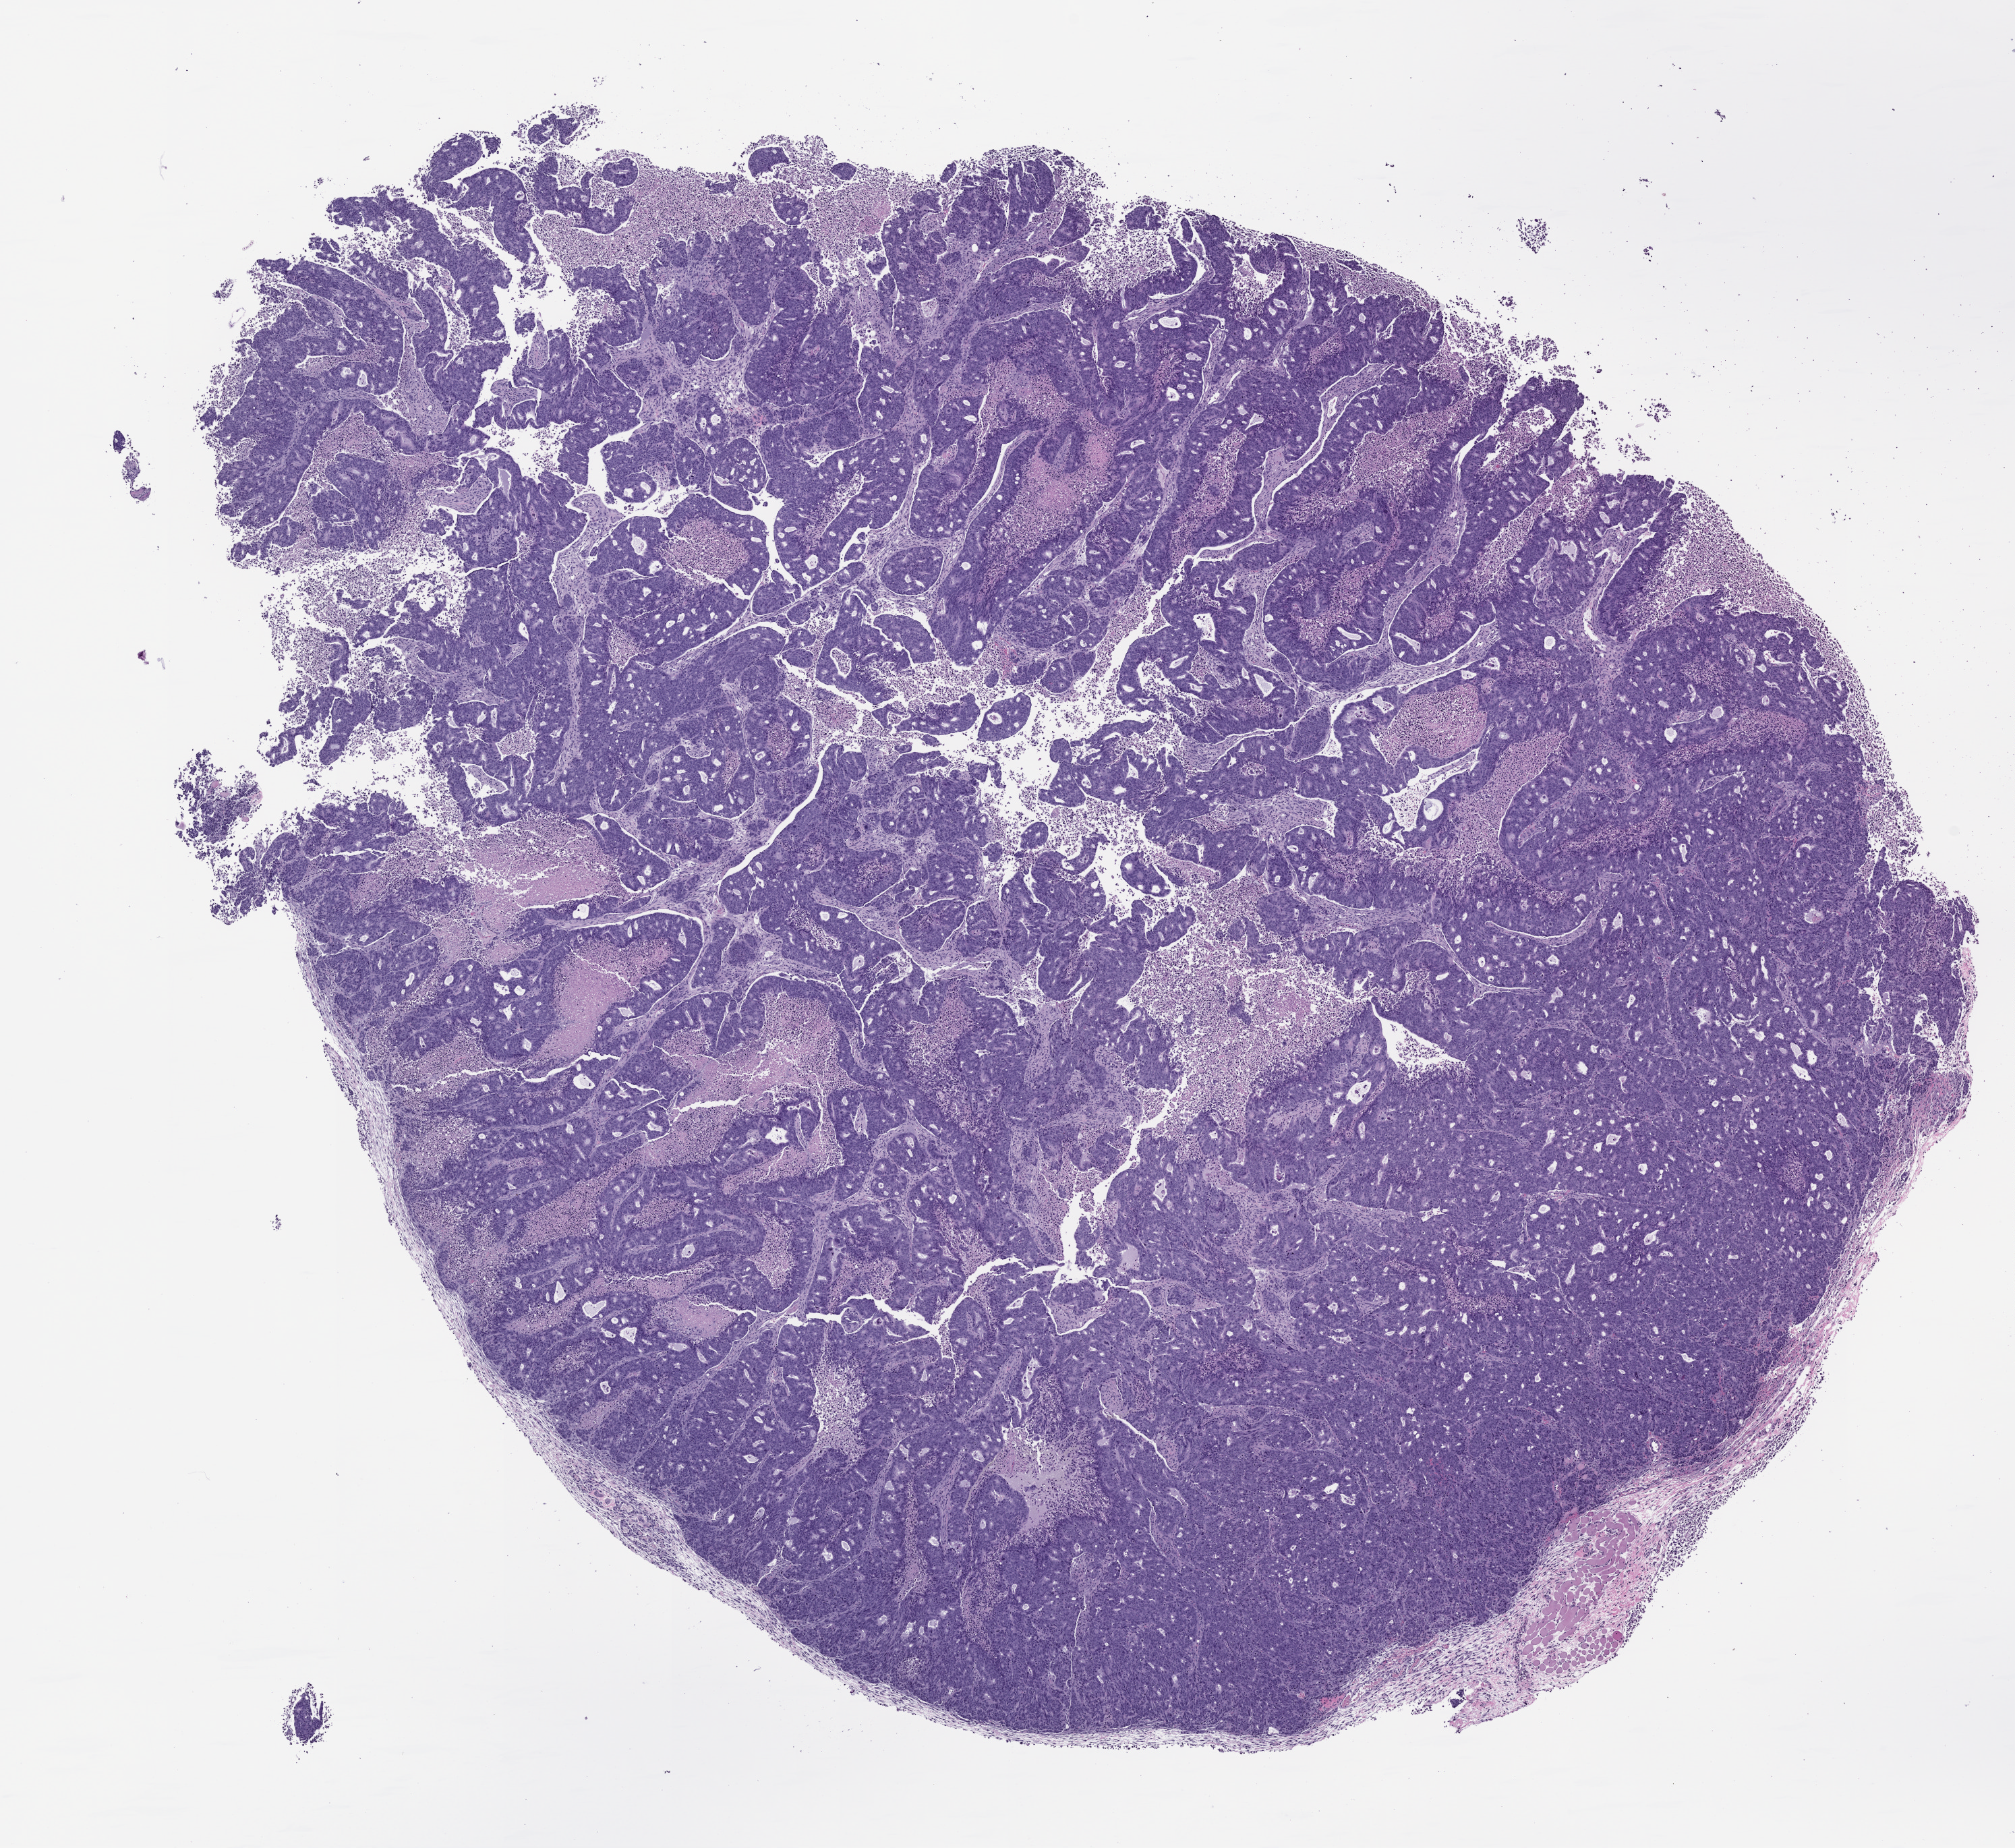
H&E whole-slide image of a patient-derived xenograft (PDX) tumor grown in a mouse, passage 1, low-resolution overview of the scanned area, about 12.0 x 11.0 mm, FFPE section, originating tumor site category: colon.
Originating patient diagnosis: Colon Adenocarcinoma.